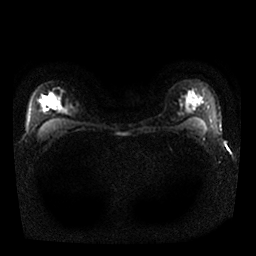
Breast MRI, one axial slice. Slice 20 of 25 in the series (ordered by position). Diffusion-weighted series; image 2 of 4 stored at this slice position (different b-values; order by instance number). 1.5 T. 4 mm slice thickness. 256 × 256 image matrix, field of view 340 × 340 mm. Female patient.
Outlined on this slice (manually delineated by an expert):
- tumour on diffusion-weighted imaging: bounding box <43,101,51,110> (left, top, right, bottom; pixels)